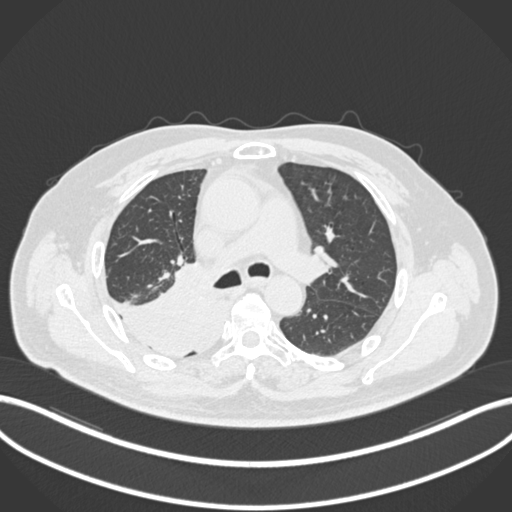
Chest CT, one axial slice; slice 127 of 218 in the series (ordered by position); reconstruction kernel B30f; 120 kVp; lung window (W 1500 / L -600 HU); 1 mm slice thickness; 512 × 512 image matrix. Male patient, age 68 years. From the clinical record (not read from this slice): clinical TNM (as recorded): T2a N0 M0.
Outlined on this slice (bounding box drawn by a radiologist):
- lung tumour (recorded histology: adenocarcinoma): box from (x=112, y=260) to (x=226, y=360) px